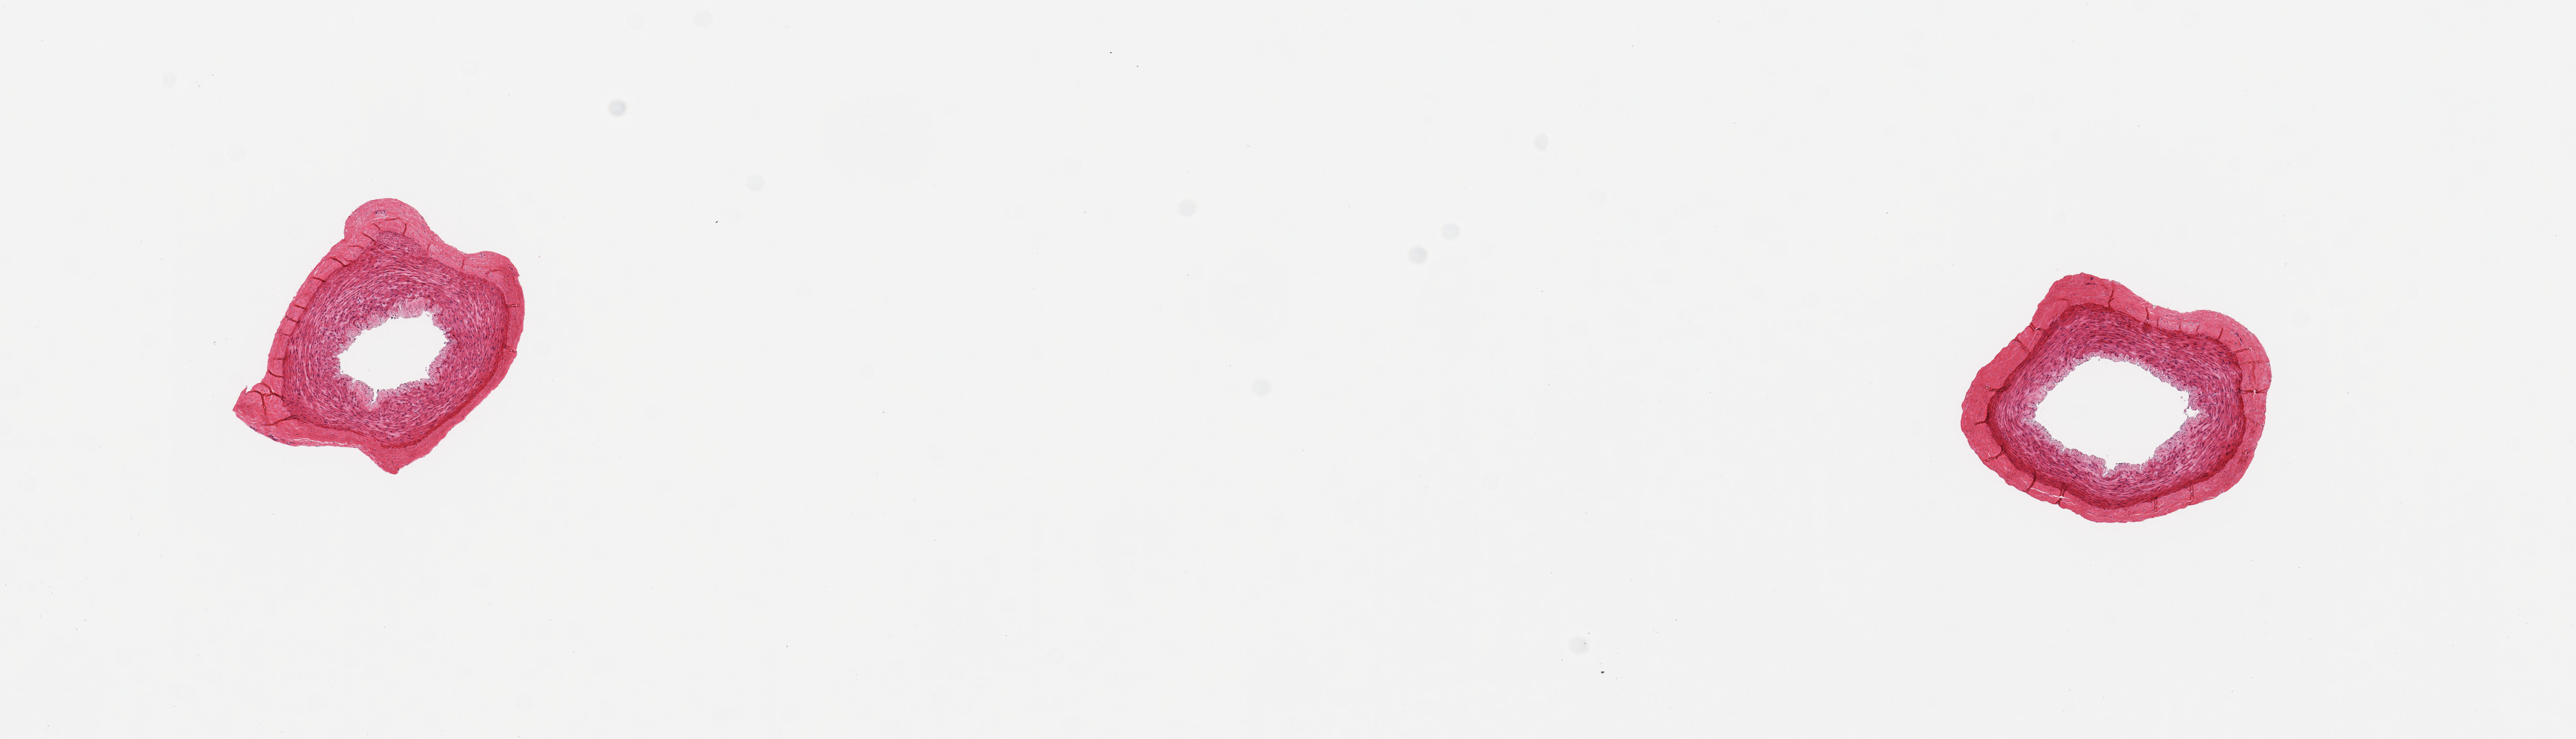
Digitized hematoxylin and eosin (H&E)-stained section — shown as a low-resolution overview of the whole scanned area (about 14.8 x 4.2 mm, from a 20x scan); PAXgene-fixed paraffin-embedded (PFPE) section; section of tibial artery (target tissue); tissue donor sample. Donor sex: male.
Review note (as recorded): 2 pieces; well trimmed.